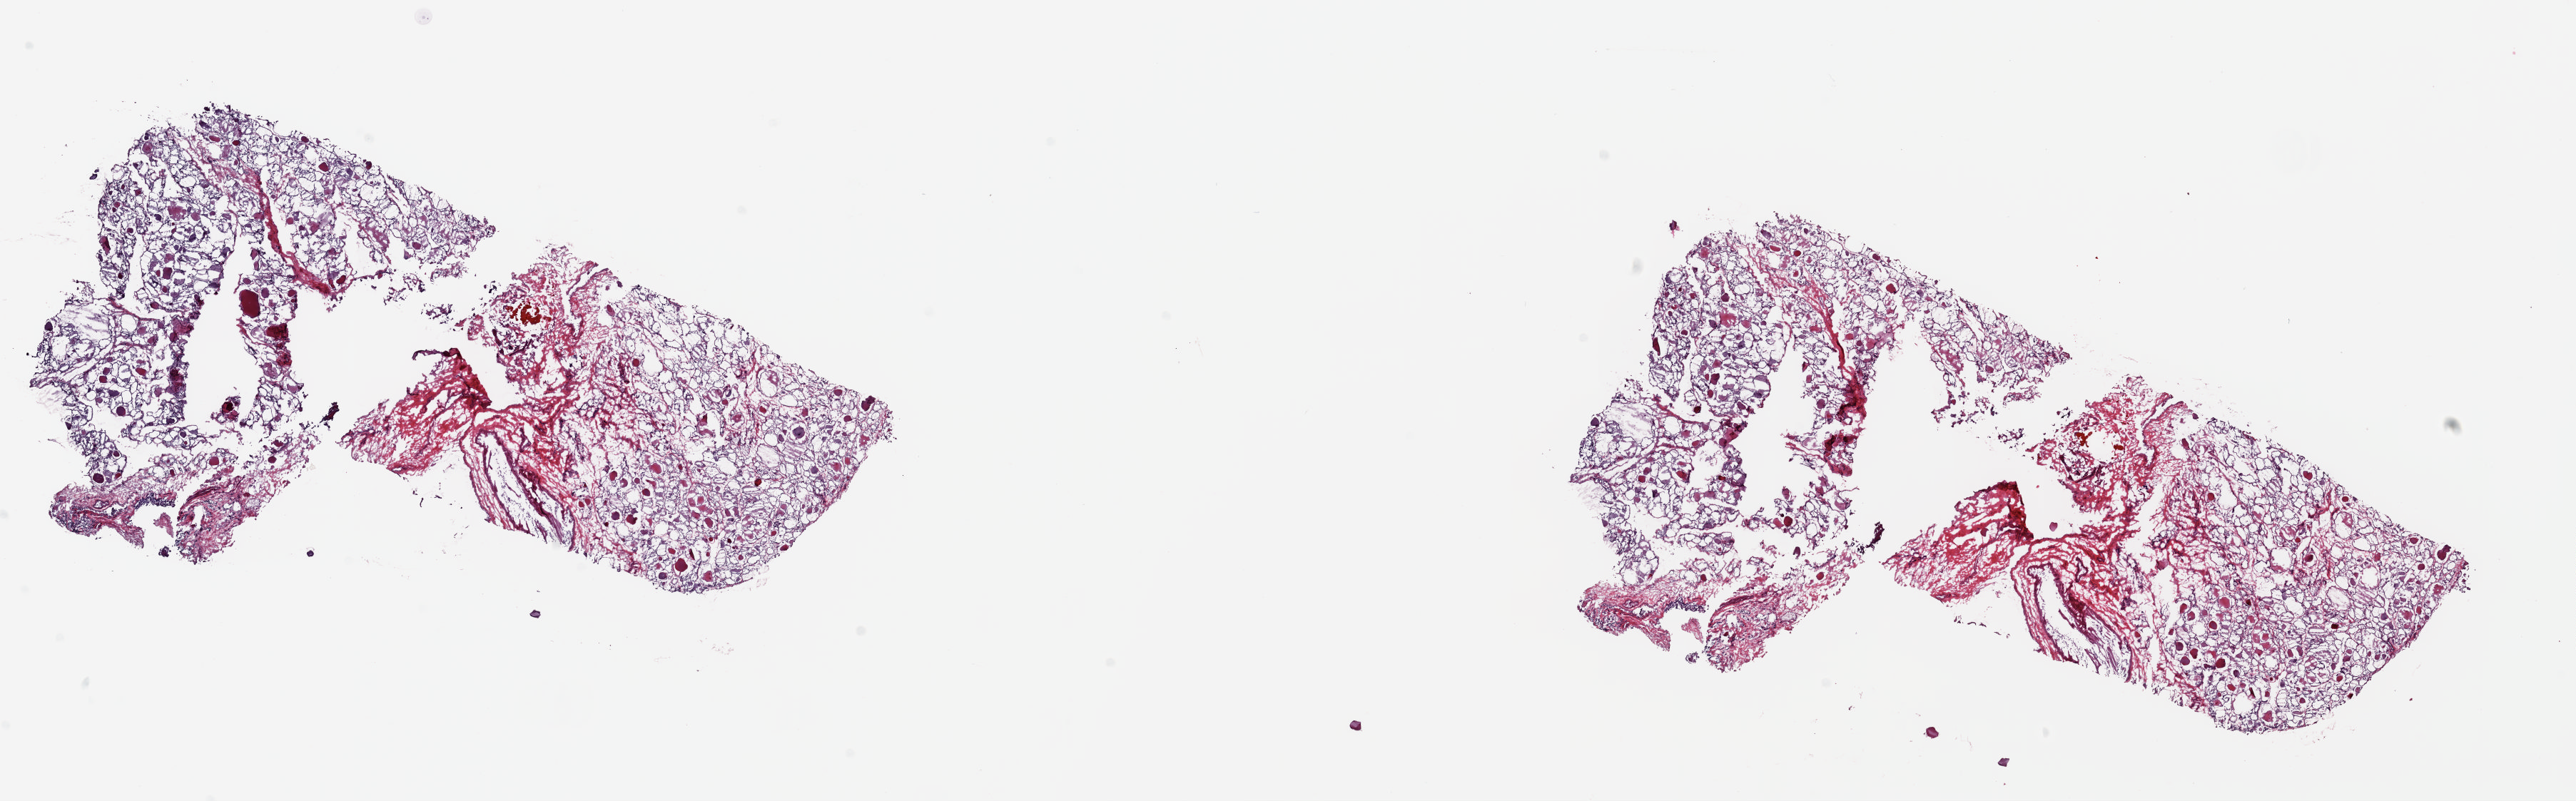
Whole-slide histology image, Hematoxylin and eosin (H&E) stained — low-resolution overview of the scanned area, about 28.5 x 8.9 mm (from a 20x scan). Frozen section. Sample: solid tissue normal (non-tumour tissue), thyroid. Patient: female, age at initial diagnosis 79 years. Pathologist review of this section (percent, as recorded): tumour cells 0%, tumour nuclei 0%, normal cells 35%, stromal cells 65%, necrosis 0%. Inflammatory infiltration, as recorded: lymphocyte infiltration 3%, monocyte infiltration 2%, neutrophil infiltration 2%.
This section: solid tissue normal sample (biorepository sample class). Patient diagnosis: Papillary adenocarcinoma, NOS (thyroid gland).